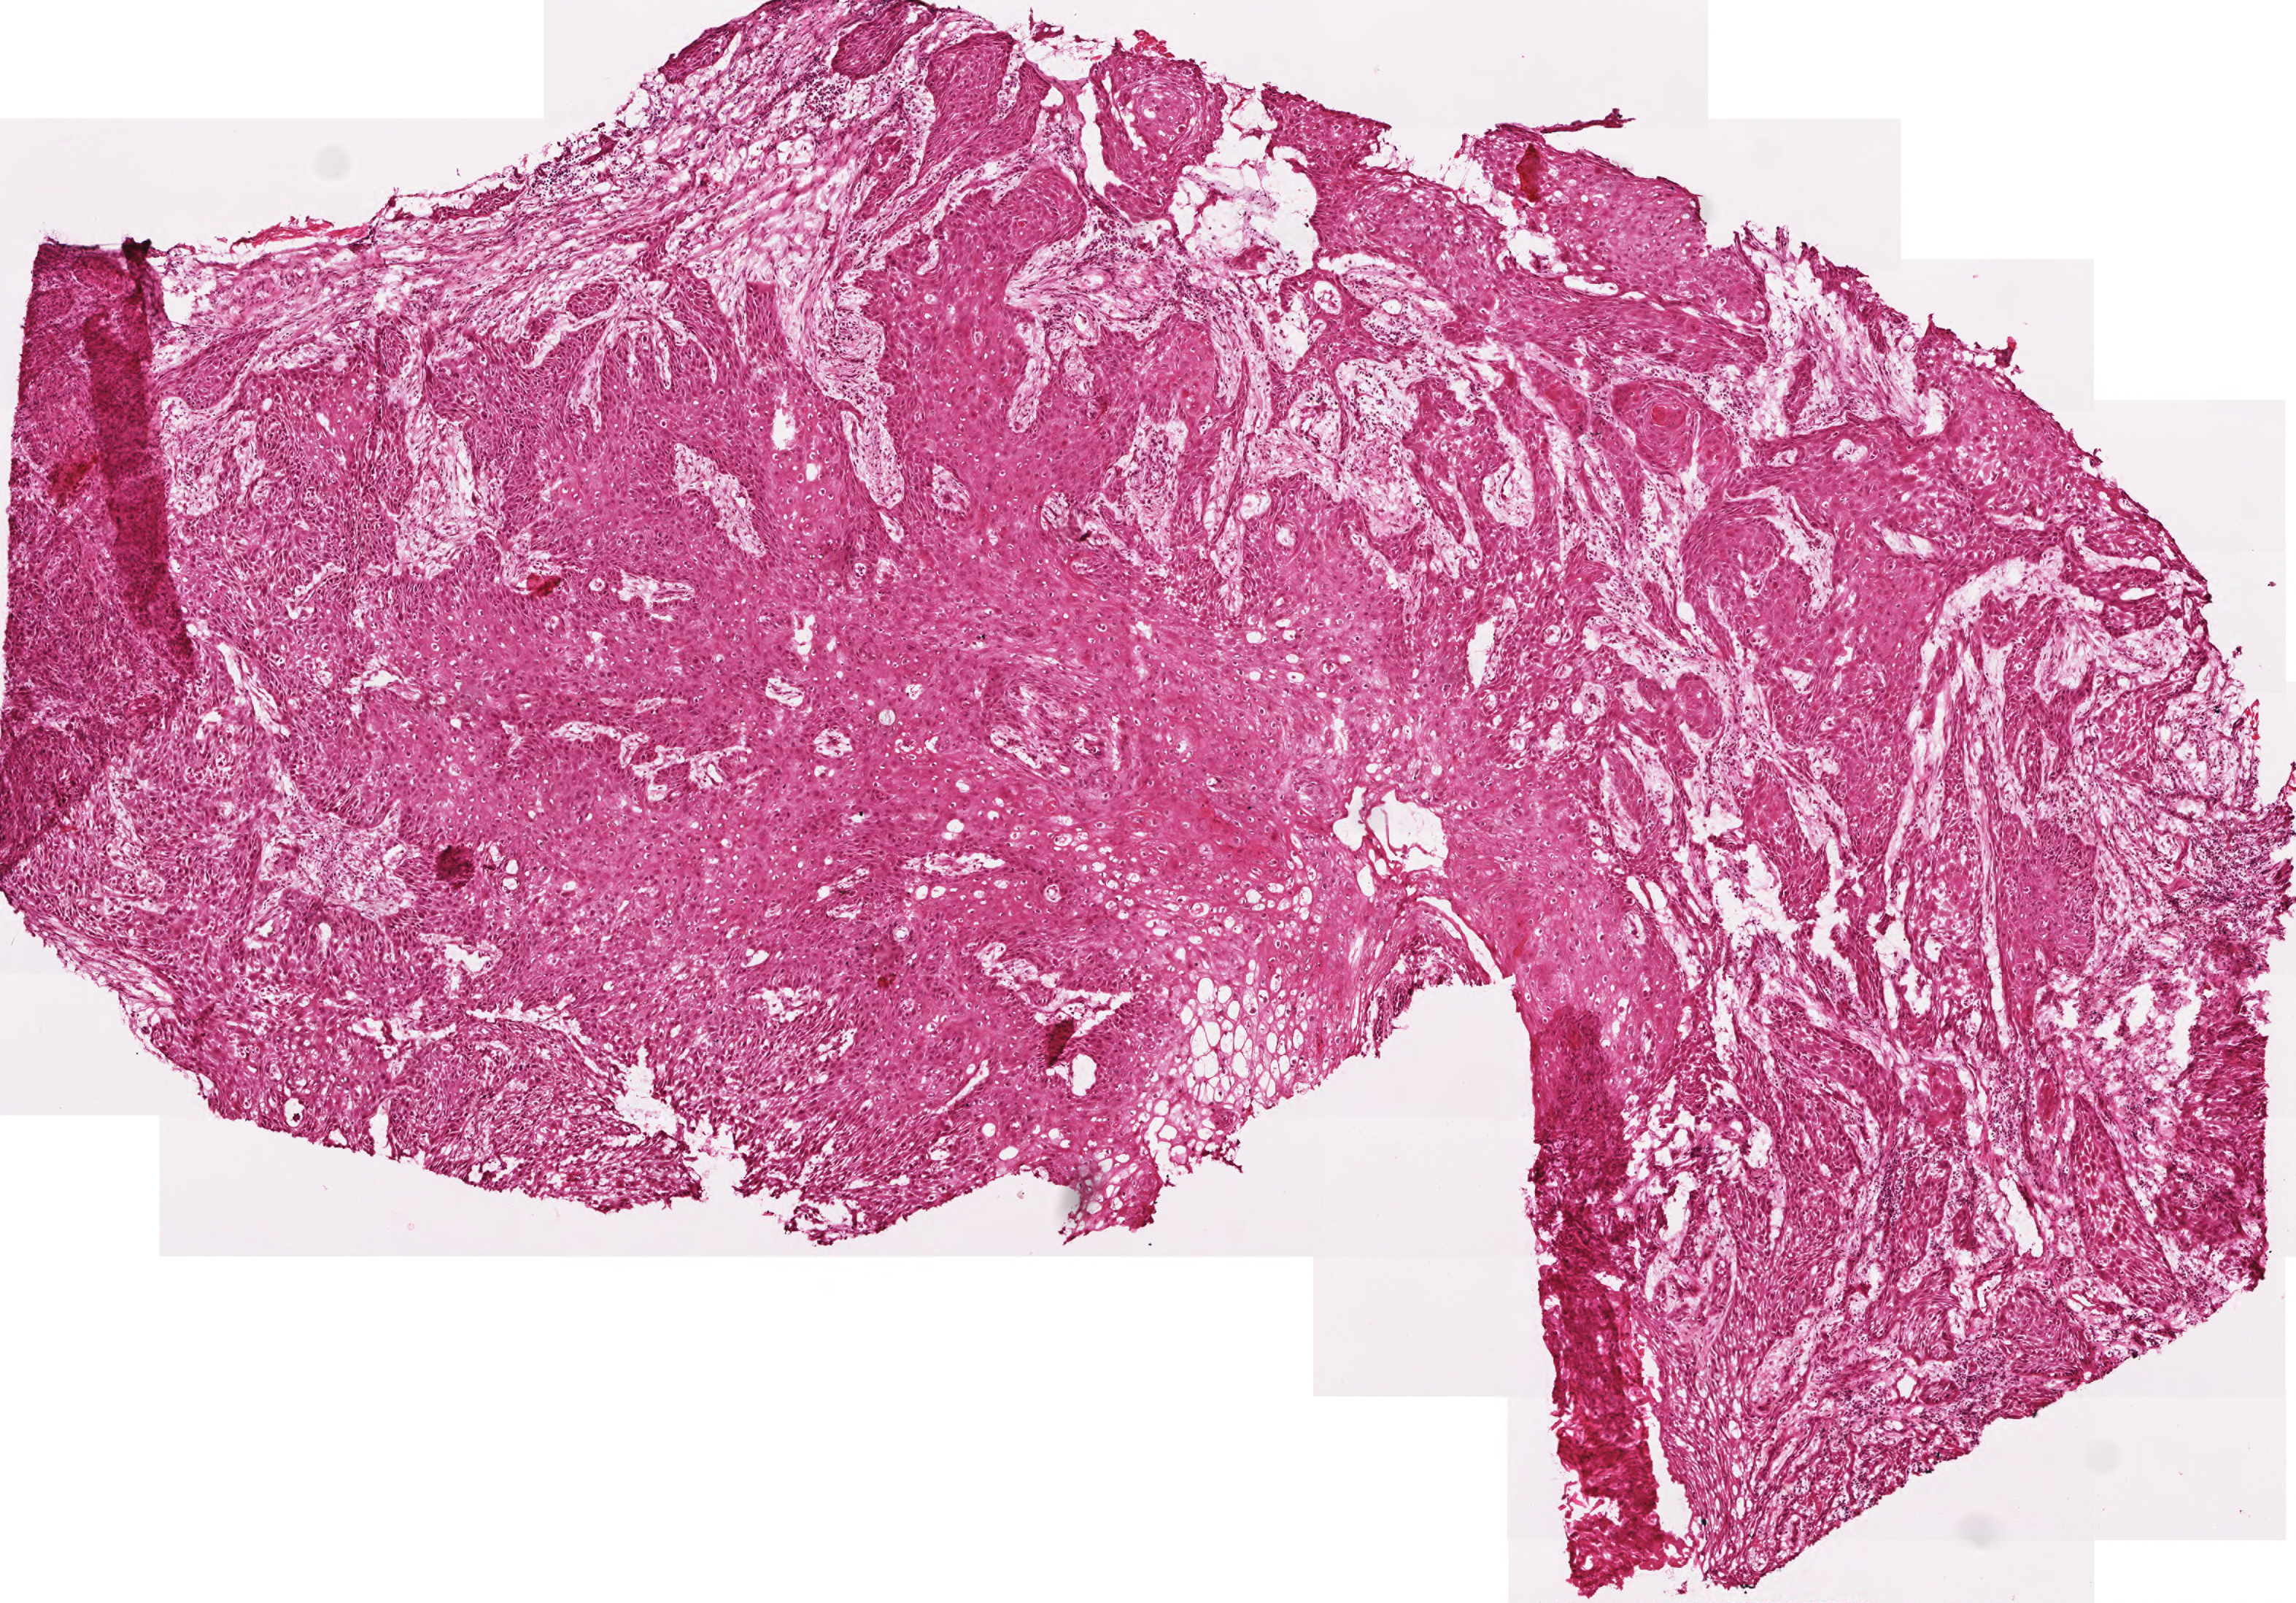
Digitized Hematoxylin and eosin (H&E) stained tissue section (whole slide) — low-resolution overview of the scanned area, about 3.1 x 2.2 mm. Frozen section. Sample: primary tumour, head and neck. Male, age 58 years at initial diagnosis.
Histologic diagnosis: Squamous cell carcinoma, NOS (overlapping lesion of lip, oral cavity and pharynx).